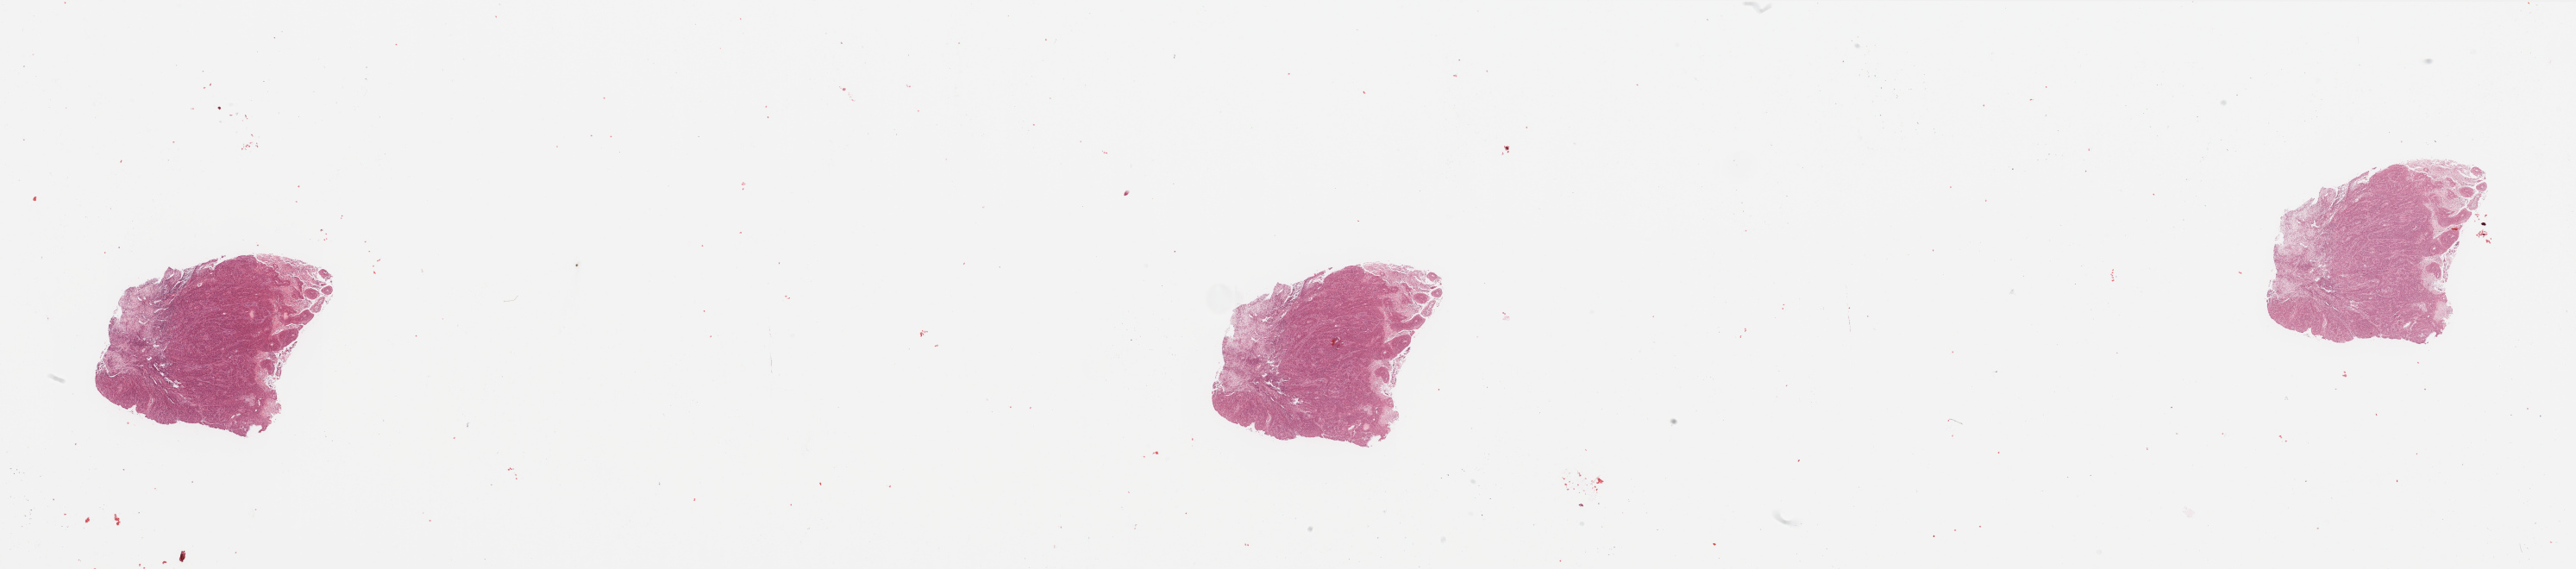
Whole-slide histology image, H&E-stained, a low-resolution overview of the entire scanned area, about 47.3 x 10.4 mm, tumour tissue sample, sampled site: floor of mouth. Patient: male, age 61 years. Histologic grade: G3 (poorly differentiated). Slide review estimates, as recorded: tumour nuclei 85%, necrosis 10%.
- primary tumour site (as recorded): oral cavity
- AJCC pathologic stage: IVB
- diagnosis: Squamous cell carcinoma, NOS (floor of mouth, NOS)